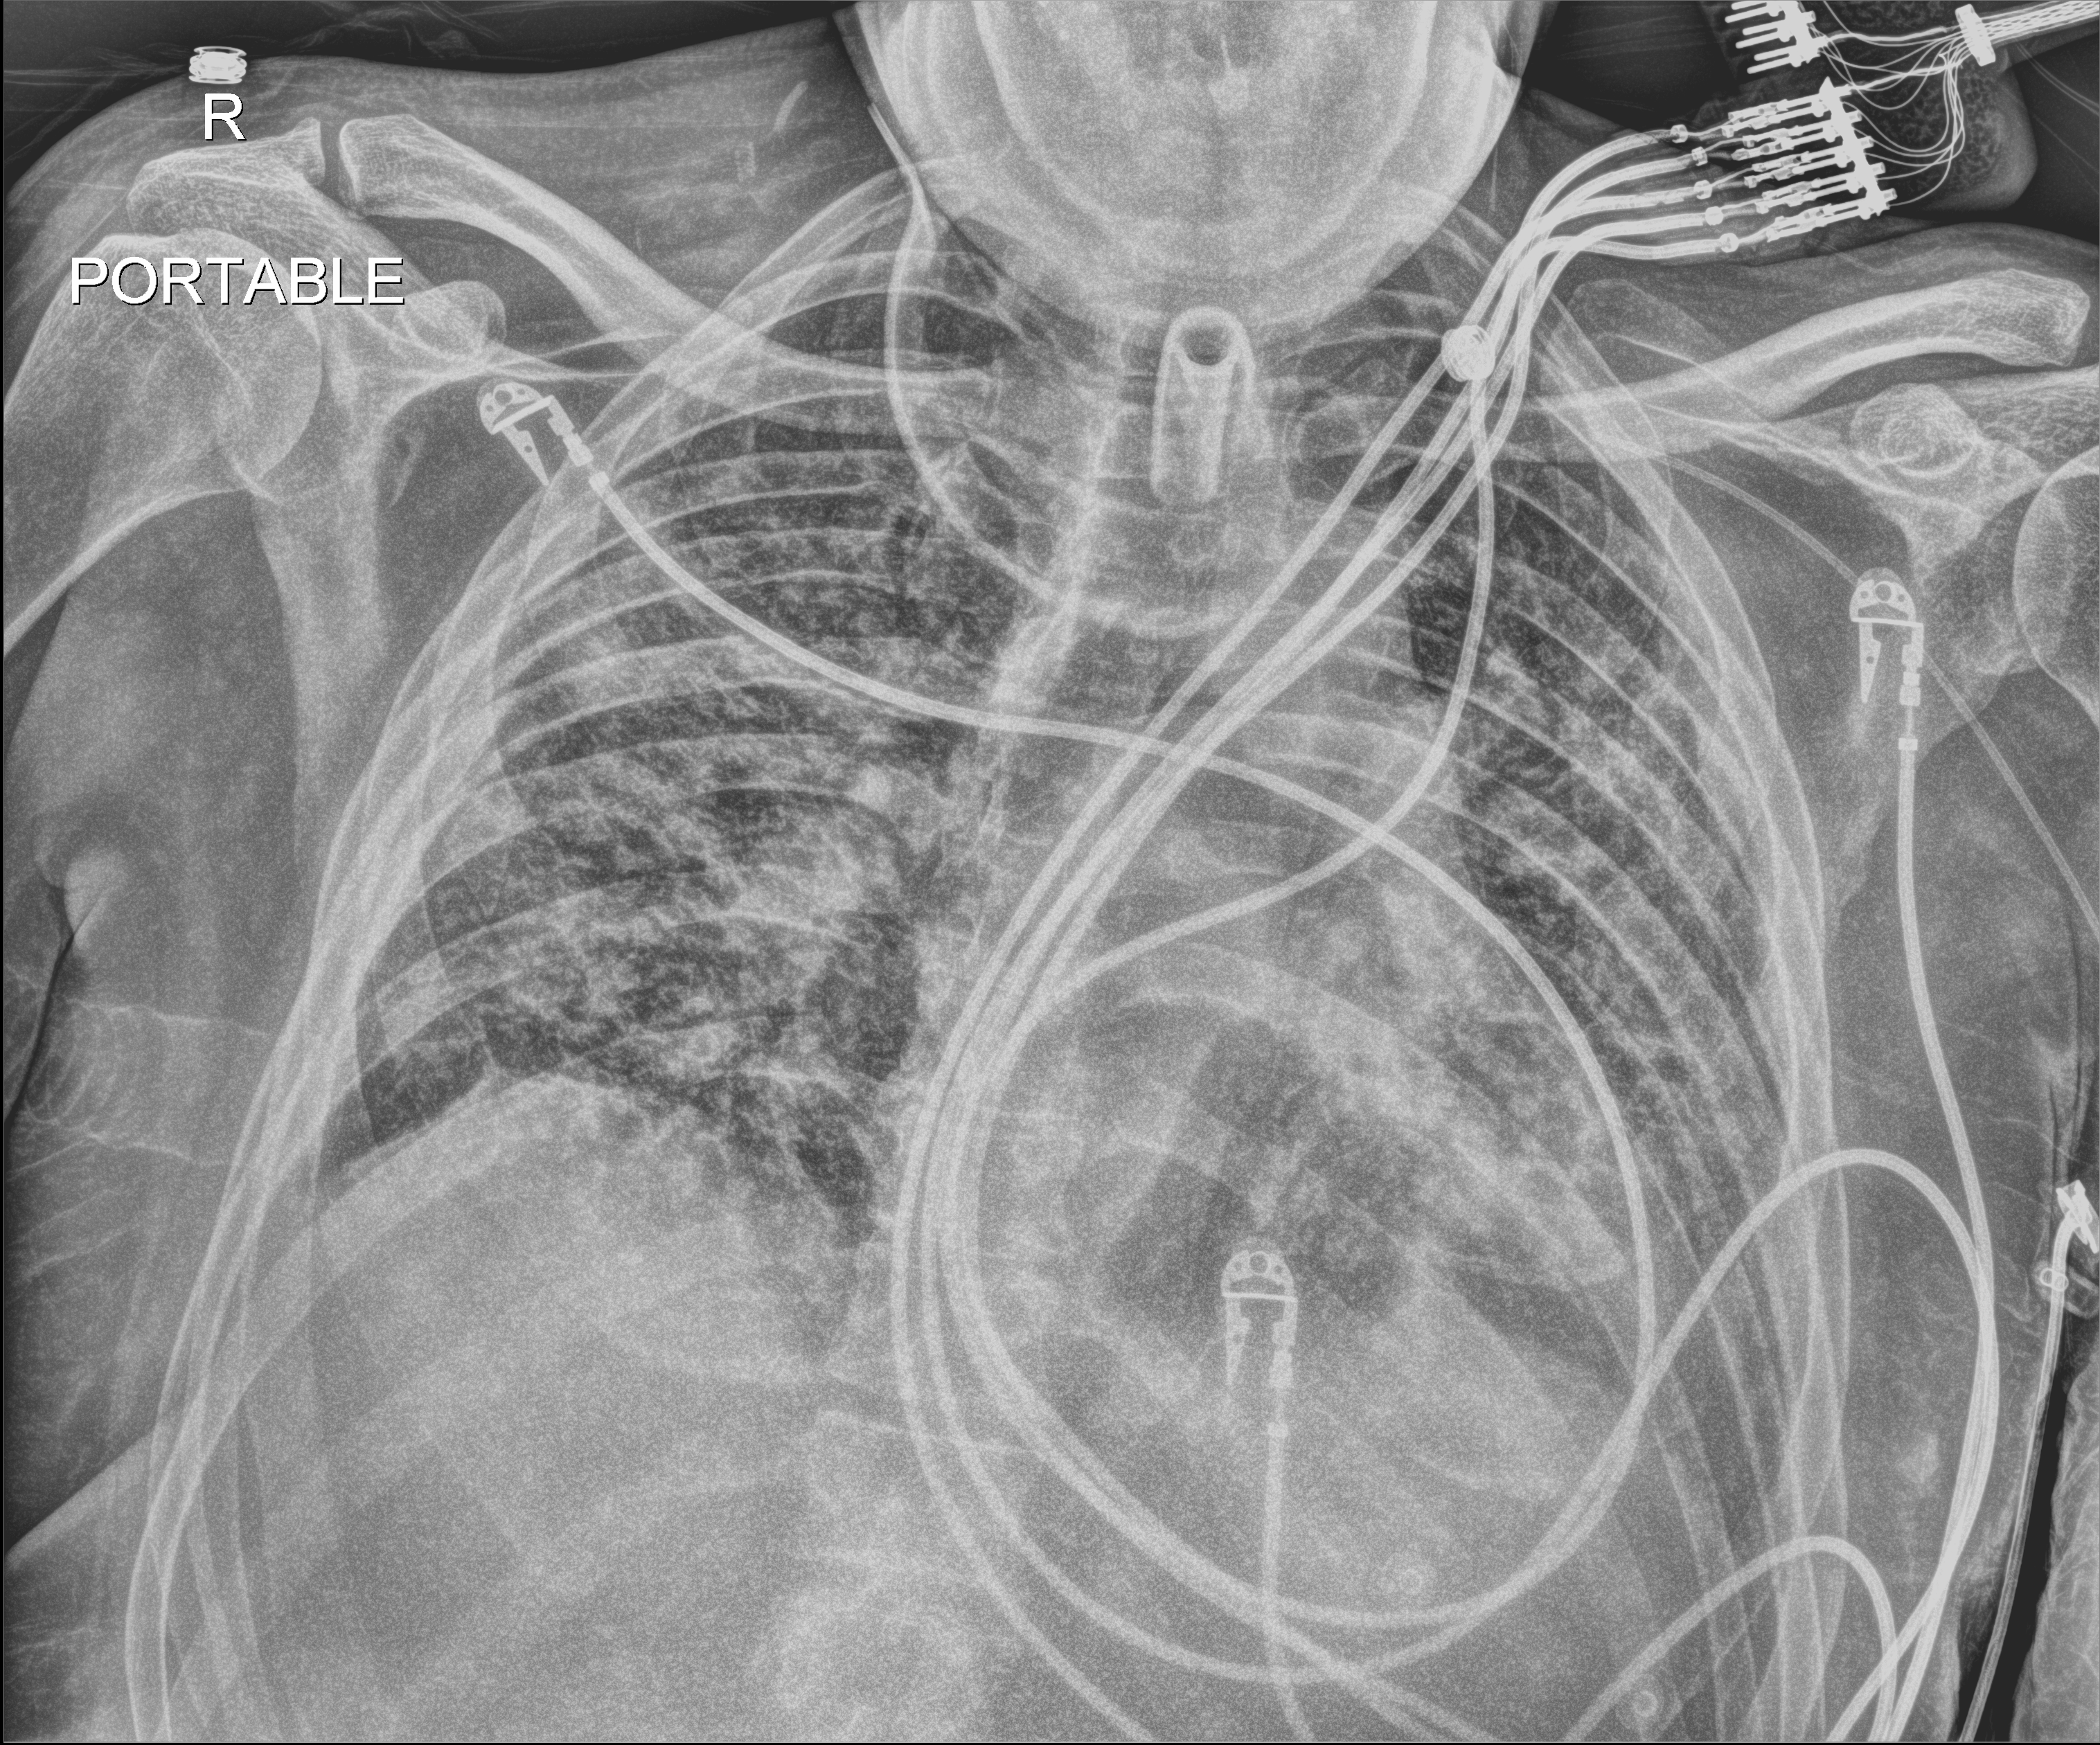
Bedside chest radiograph (digital radiography); anteroposterior (AP) projection. Male patient hospitalised with COVID-19, age 18–59 years.
Hospital-stay facts (about this admission, not read from this image; timing relative to this image not recorded):
- mechanically ventilated during this hospital stay: yes
- length of hospital stay: 75 days
- admitted to intensive care during this hospital stay: yes